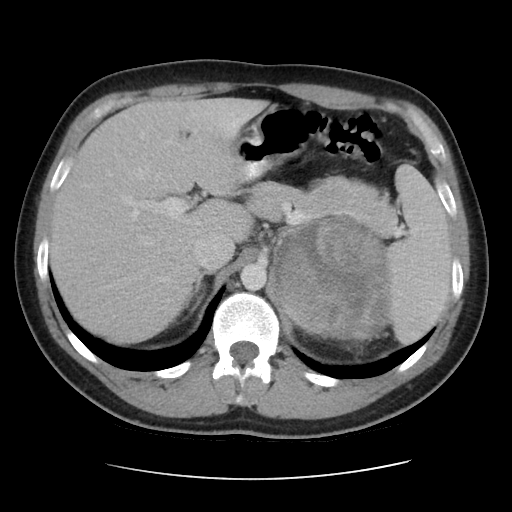
Contrast-enhanced abdominal CT, one axial slice. Position 31 of 48 along the scan axis. 120 kVp. Intravenous contrast given. Soft-tissue window (W 400 / L 40 HU). 5 mm slice thickness. 512 × 512 image matrix, field of view 360 × 360 mm. Male patient, age 32 years. From the clinical record (not read from this slice): diagnosis: adrenocortical carcinoma; tumour side: left adrenal; tumour size at pathology: 14 cm; Ki-67 index: 67 %; stage (as recorded): 3.
Annotated regions visible in this slice (semi-automatic segmentation, software-assisted and operator-edited):
- mass: box from (x=278, y=219) to (x=389, y=337) px